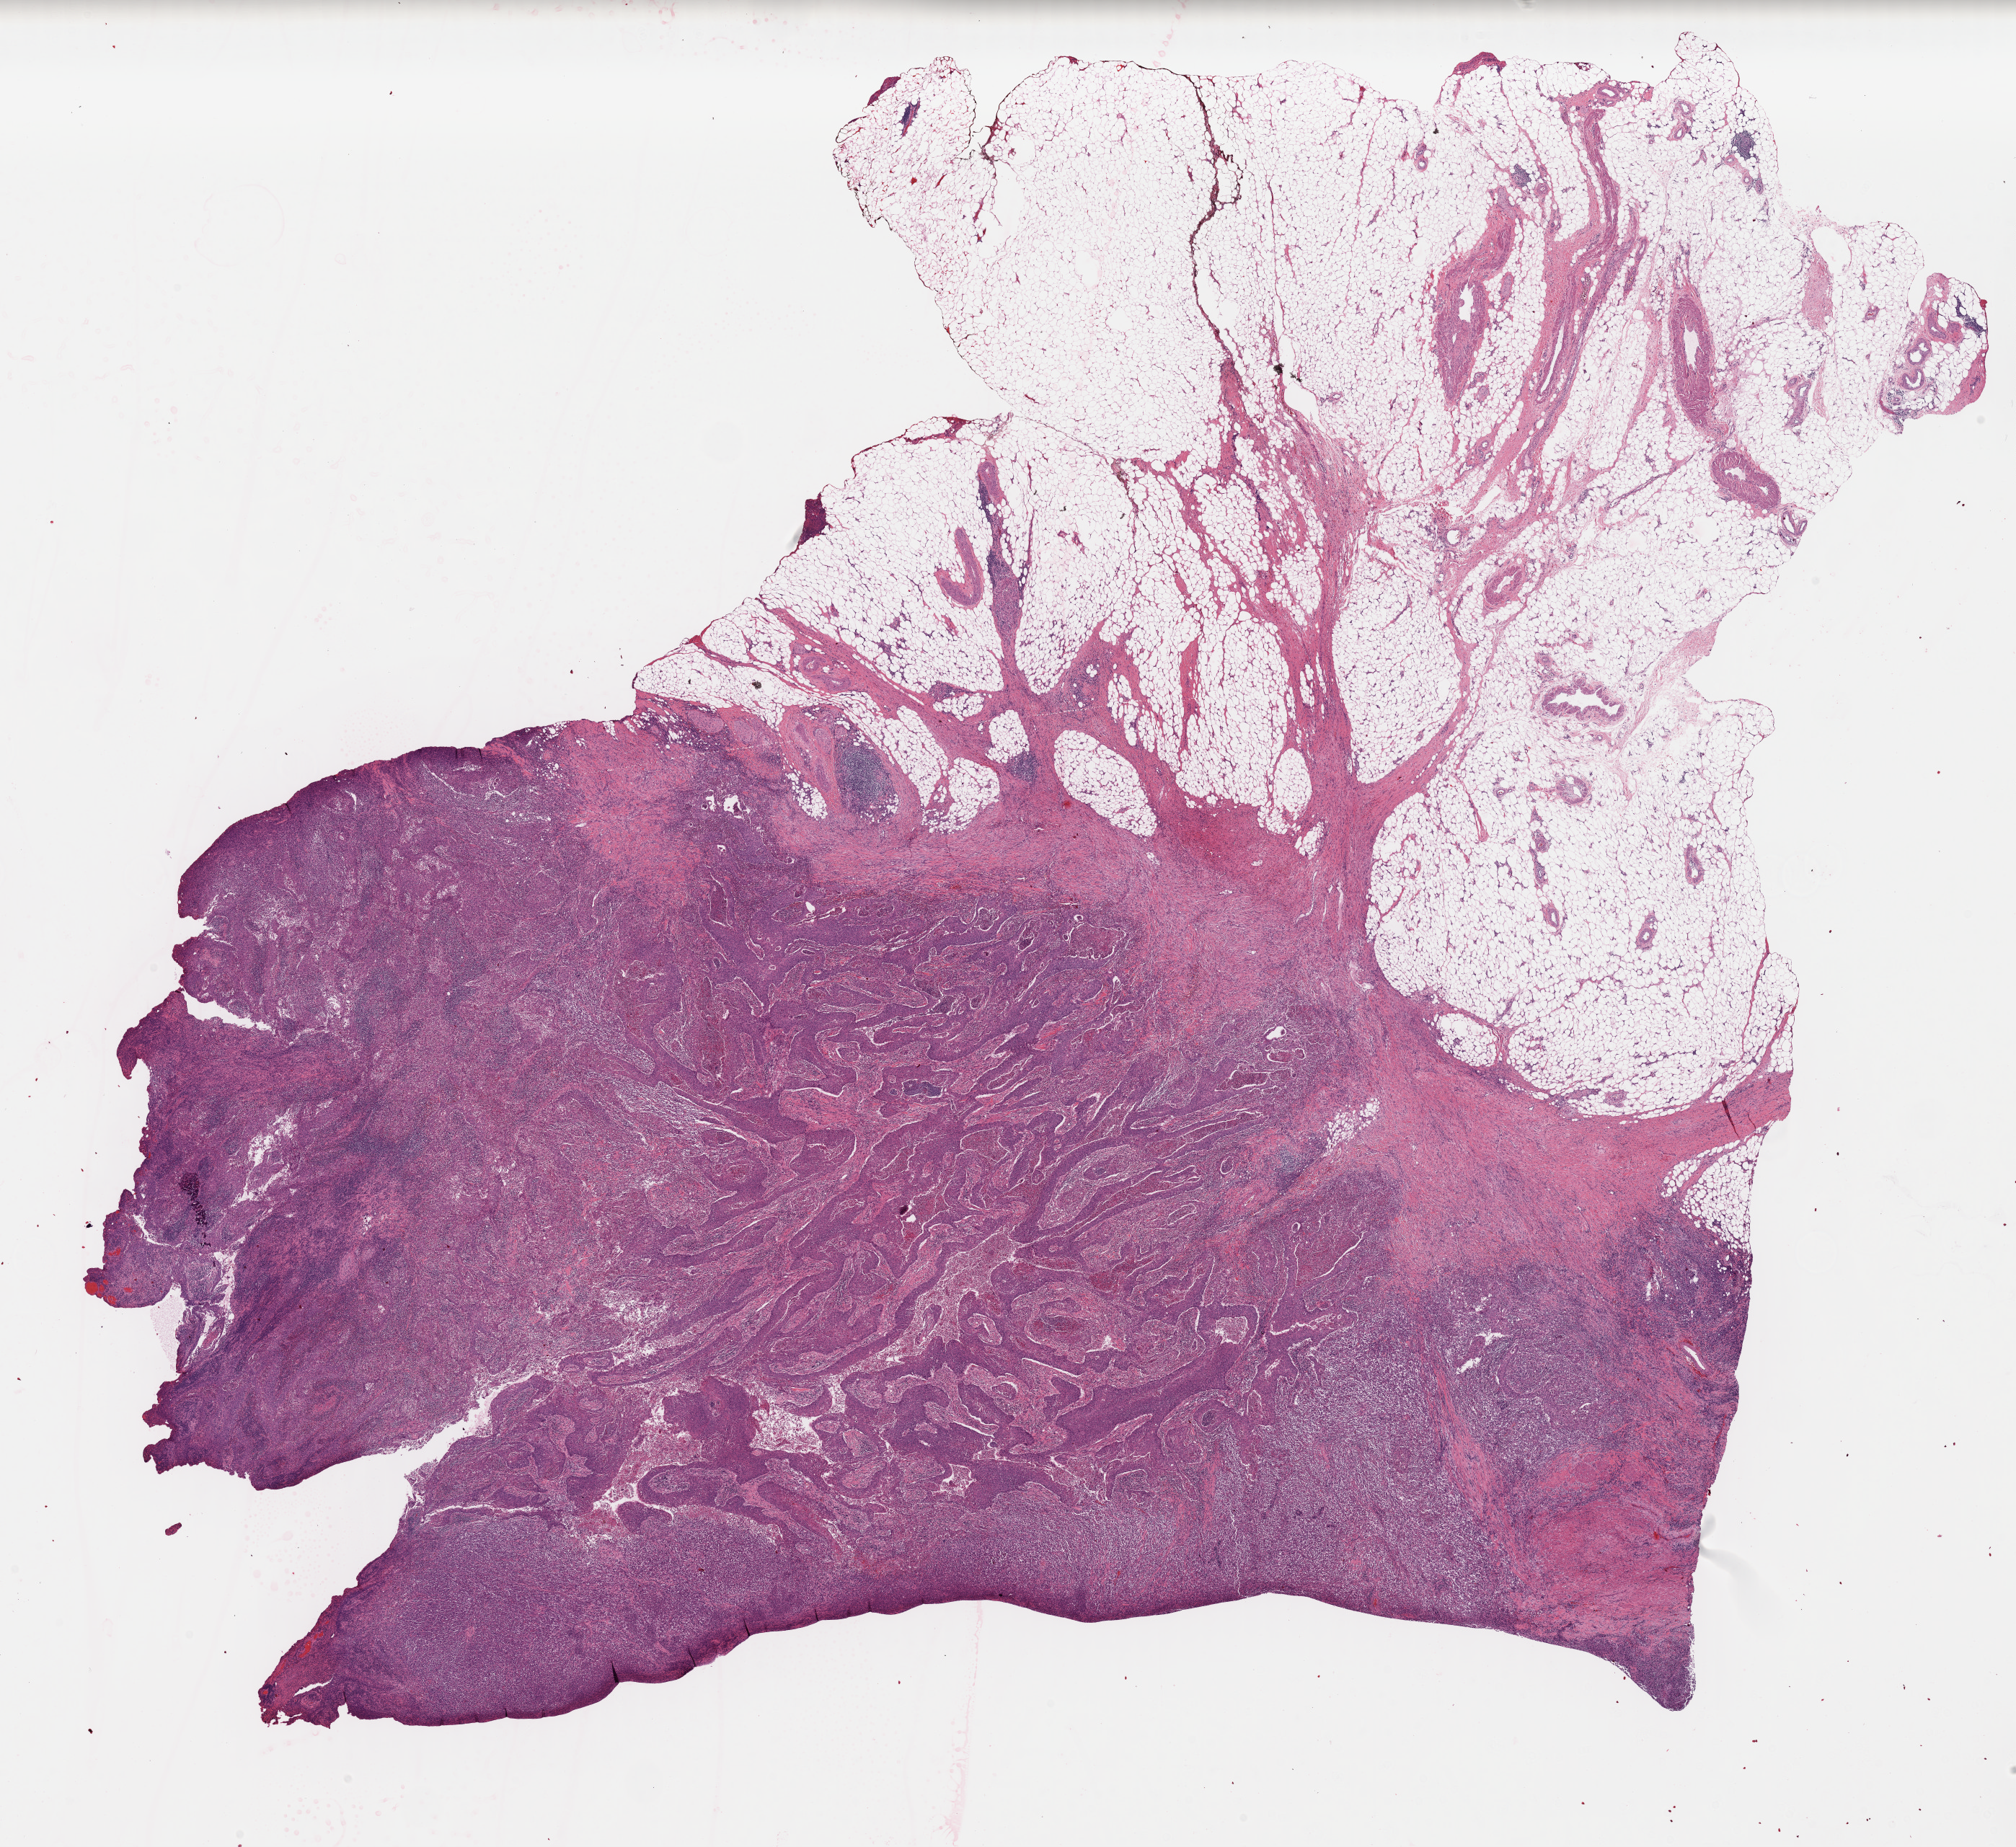
Whole-slide histology image, H&E-stained — a low-resolution overview of the entire scanned area, about 22.1 x 20.2 mm; formalin-fixed paraffin-embedded (FFPE) diagnostic section; bladder, primary tumour sample. Male patient; age at initial diagnosis 75 years. Histologic grade: high grade.
TNM: T3a N0 MX. Lymph nodes positive (case pathology): 0 of 13 examined. AJCC pathologic stage: III (6th edition). Pathologic diagnosis: Transitional cell carcinoma (lateral wall of bladder).